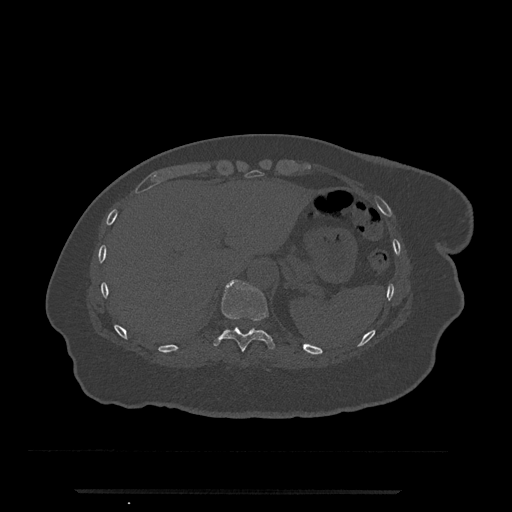
CT including the spine, one axial slice. Slice 278 of 797 in the series (ordered by position). Reconstruction kernel Br40s/3. Bone window (W 1800 / L 400 HU). 512 × 512 image matrix, field of view 440 × 440 mm. Patient: female, 51 years. From the clinical record (not read from this slice): primary cancer: neuro.
Structures marked on this image (semi-automatic segmentation, software-assisted and operator-edited):
- T10 vertebra: bounding box (x1, y1, x2, y2) in pixels: (213, 279, 275, 352)